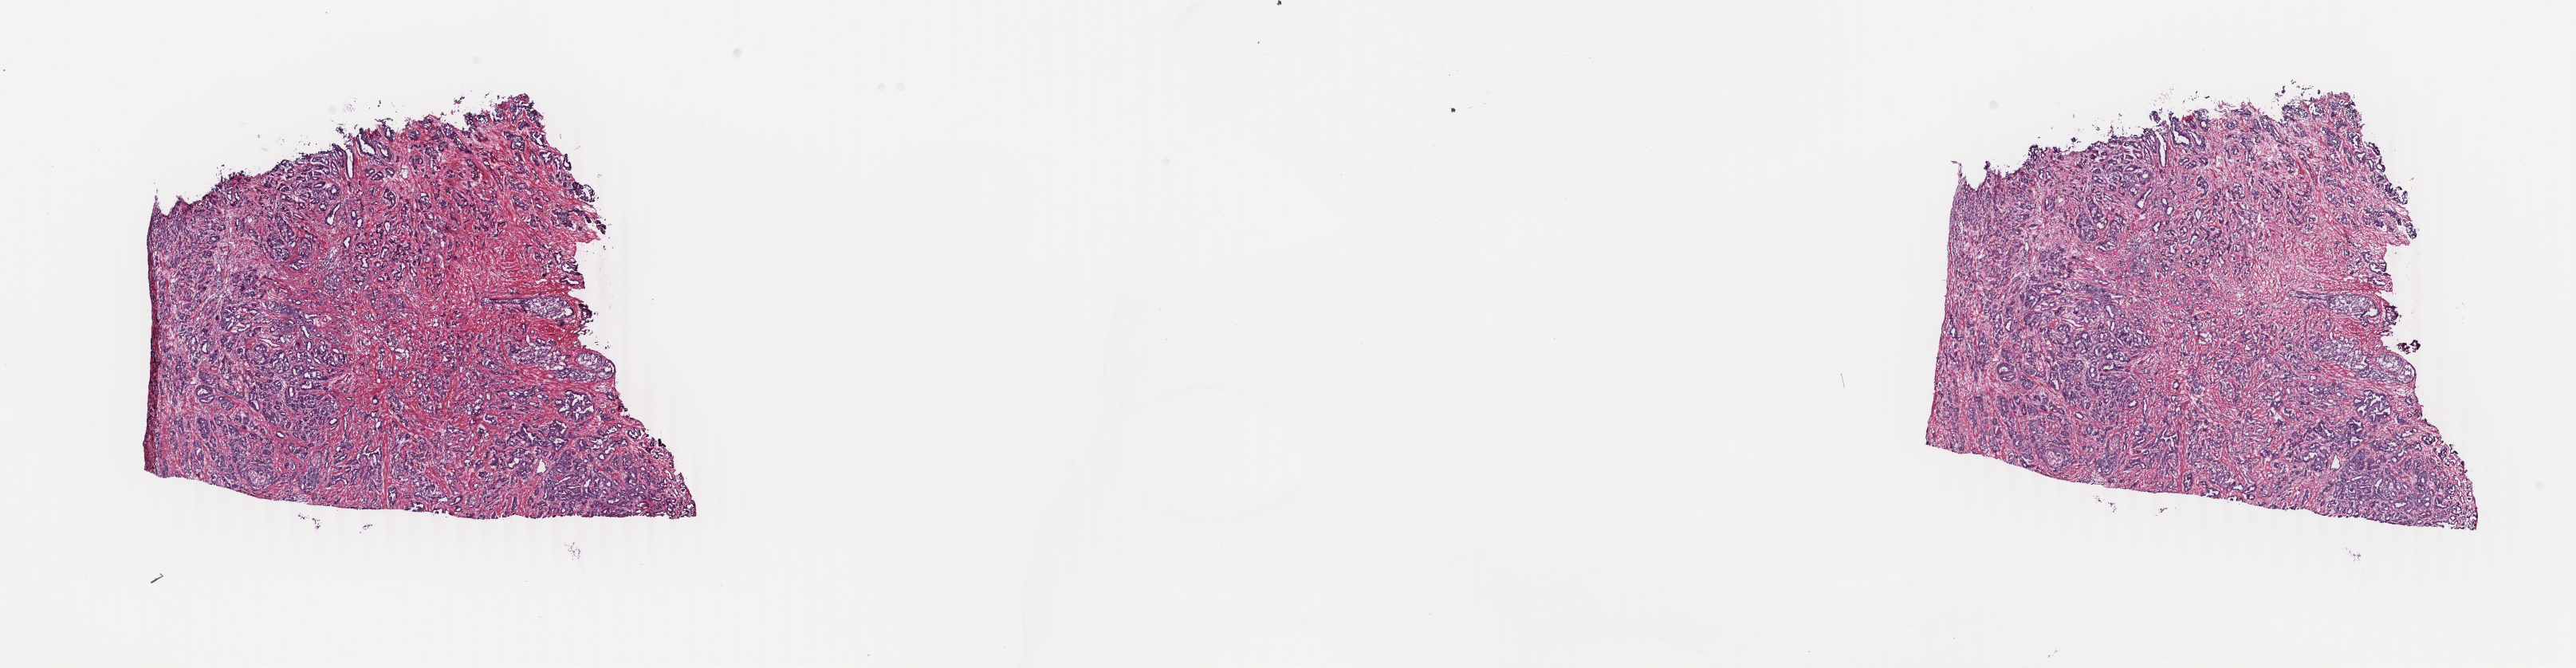
Whole-slide histology image, H&E-stained, whole scanned area (about 25.7 x 6.7 mm) shown as a low-resolution overview; frozen section from the top of the tissue portion; primary tumour sample from the prostate. Male, age 63 years at initial diagnosis. Gleason score: 8 (4+4). Slide review estimates, as recorded: tumour cells 70%, tumour nuclei 80%, normal cells 10%, stromal cells 20%, necrosis 0%. Infiltration values recorded for this section: lymphocyte infiltration 0%, monocyte infiltration 0%, neutrophil infiltration 0%.
- laterality: bilateral
- lymph nodes positive (case pathology): 0 of 12 examined
- histologic diagnosis: Infiltrating duct carcinoma, NOS (prostate gland)